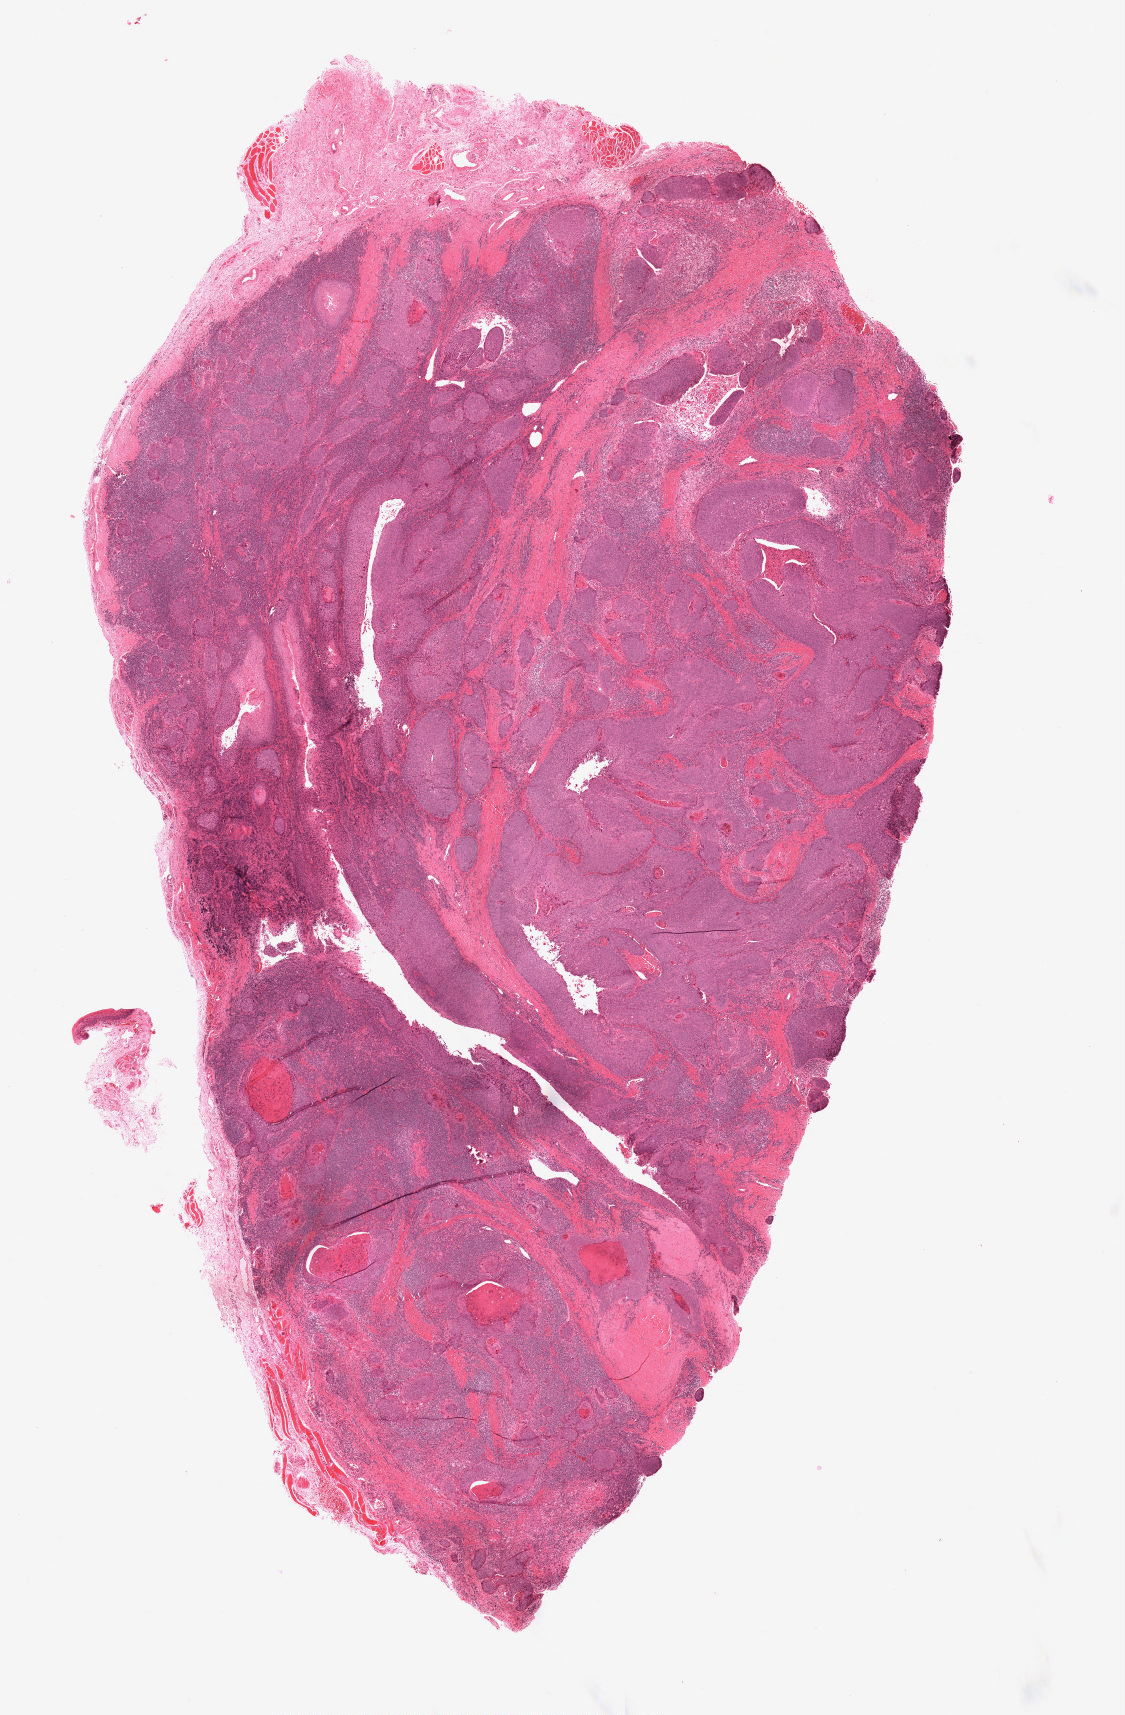
Whole-slide histology image, Hematoxylin and eosin (H&E) stained, low-resolution overview of the scanned area, about 9.0 x 13.7 mm (slide scanned at 20x); FFPE section; head and neck, primary tumour sample. Female patient; age at initial diagnosis 53 years. Histologic grade: G2 (moderately differentiated).
* AJCC pathologic stage: IVA (7th edition)
* pathologic diagnosis: Squamous cell carcinoma, NOS (tonsil, NOS)
* laterality: right